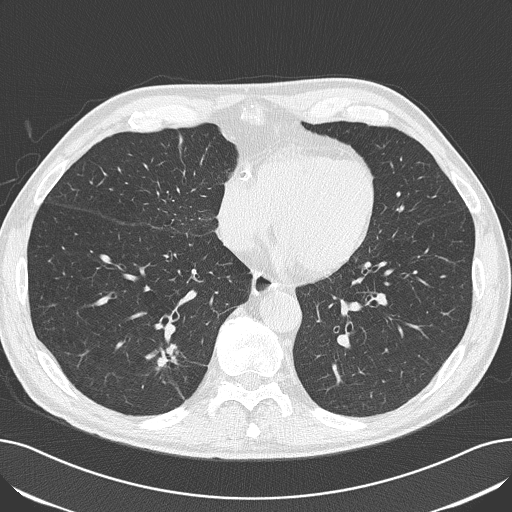
Low-dose screening chest CT, one axial slice; slice 63 of 182 in the series (ordered by position); lung window (W 1500 / L -600 HU); 512 × 512 image matrix, field of view 368 × 368 mm.
Outlined on this slice (outlined manually by an expert reader):
- lesion 1 (tumor, lower lobe of right lung): box from (x=157, y=345) to (x=177, y=368) px